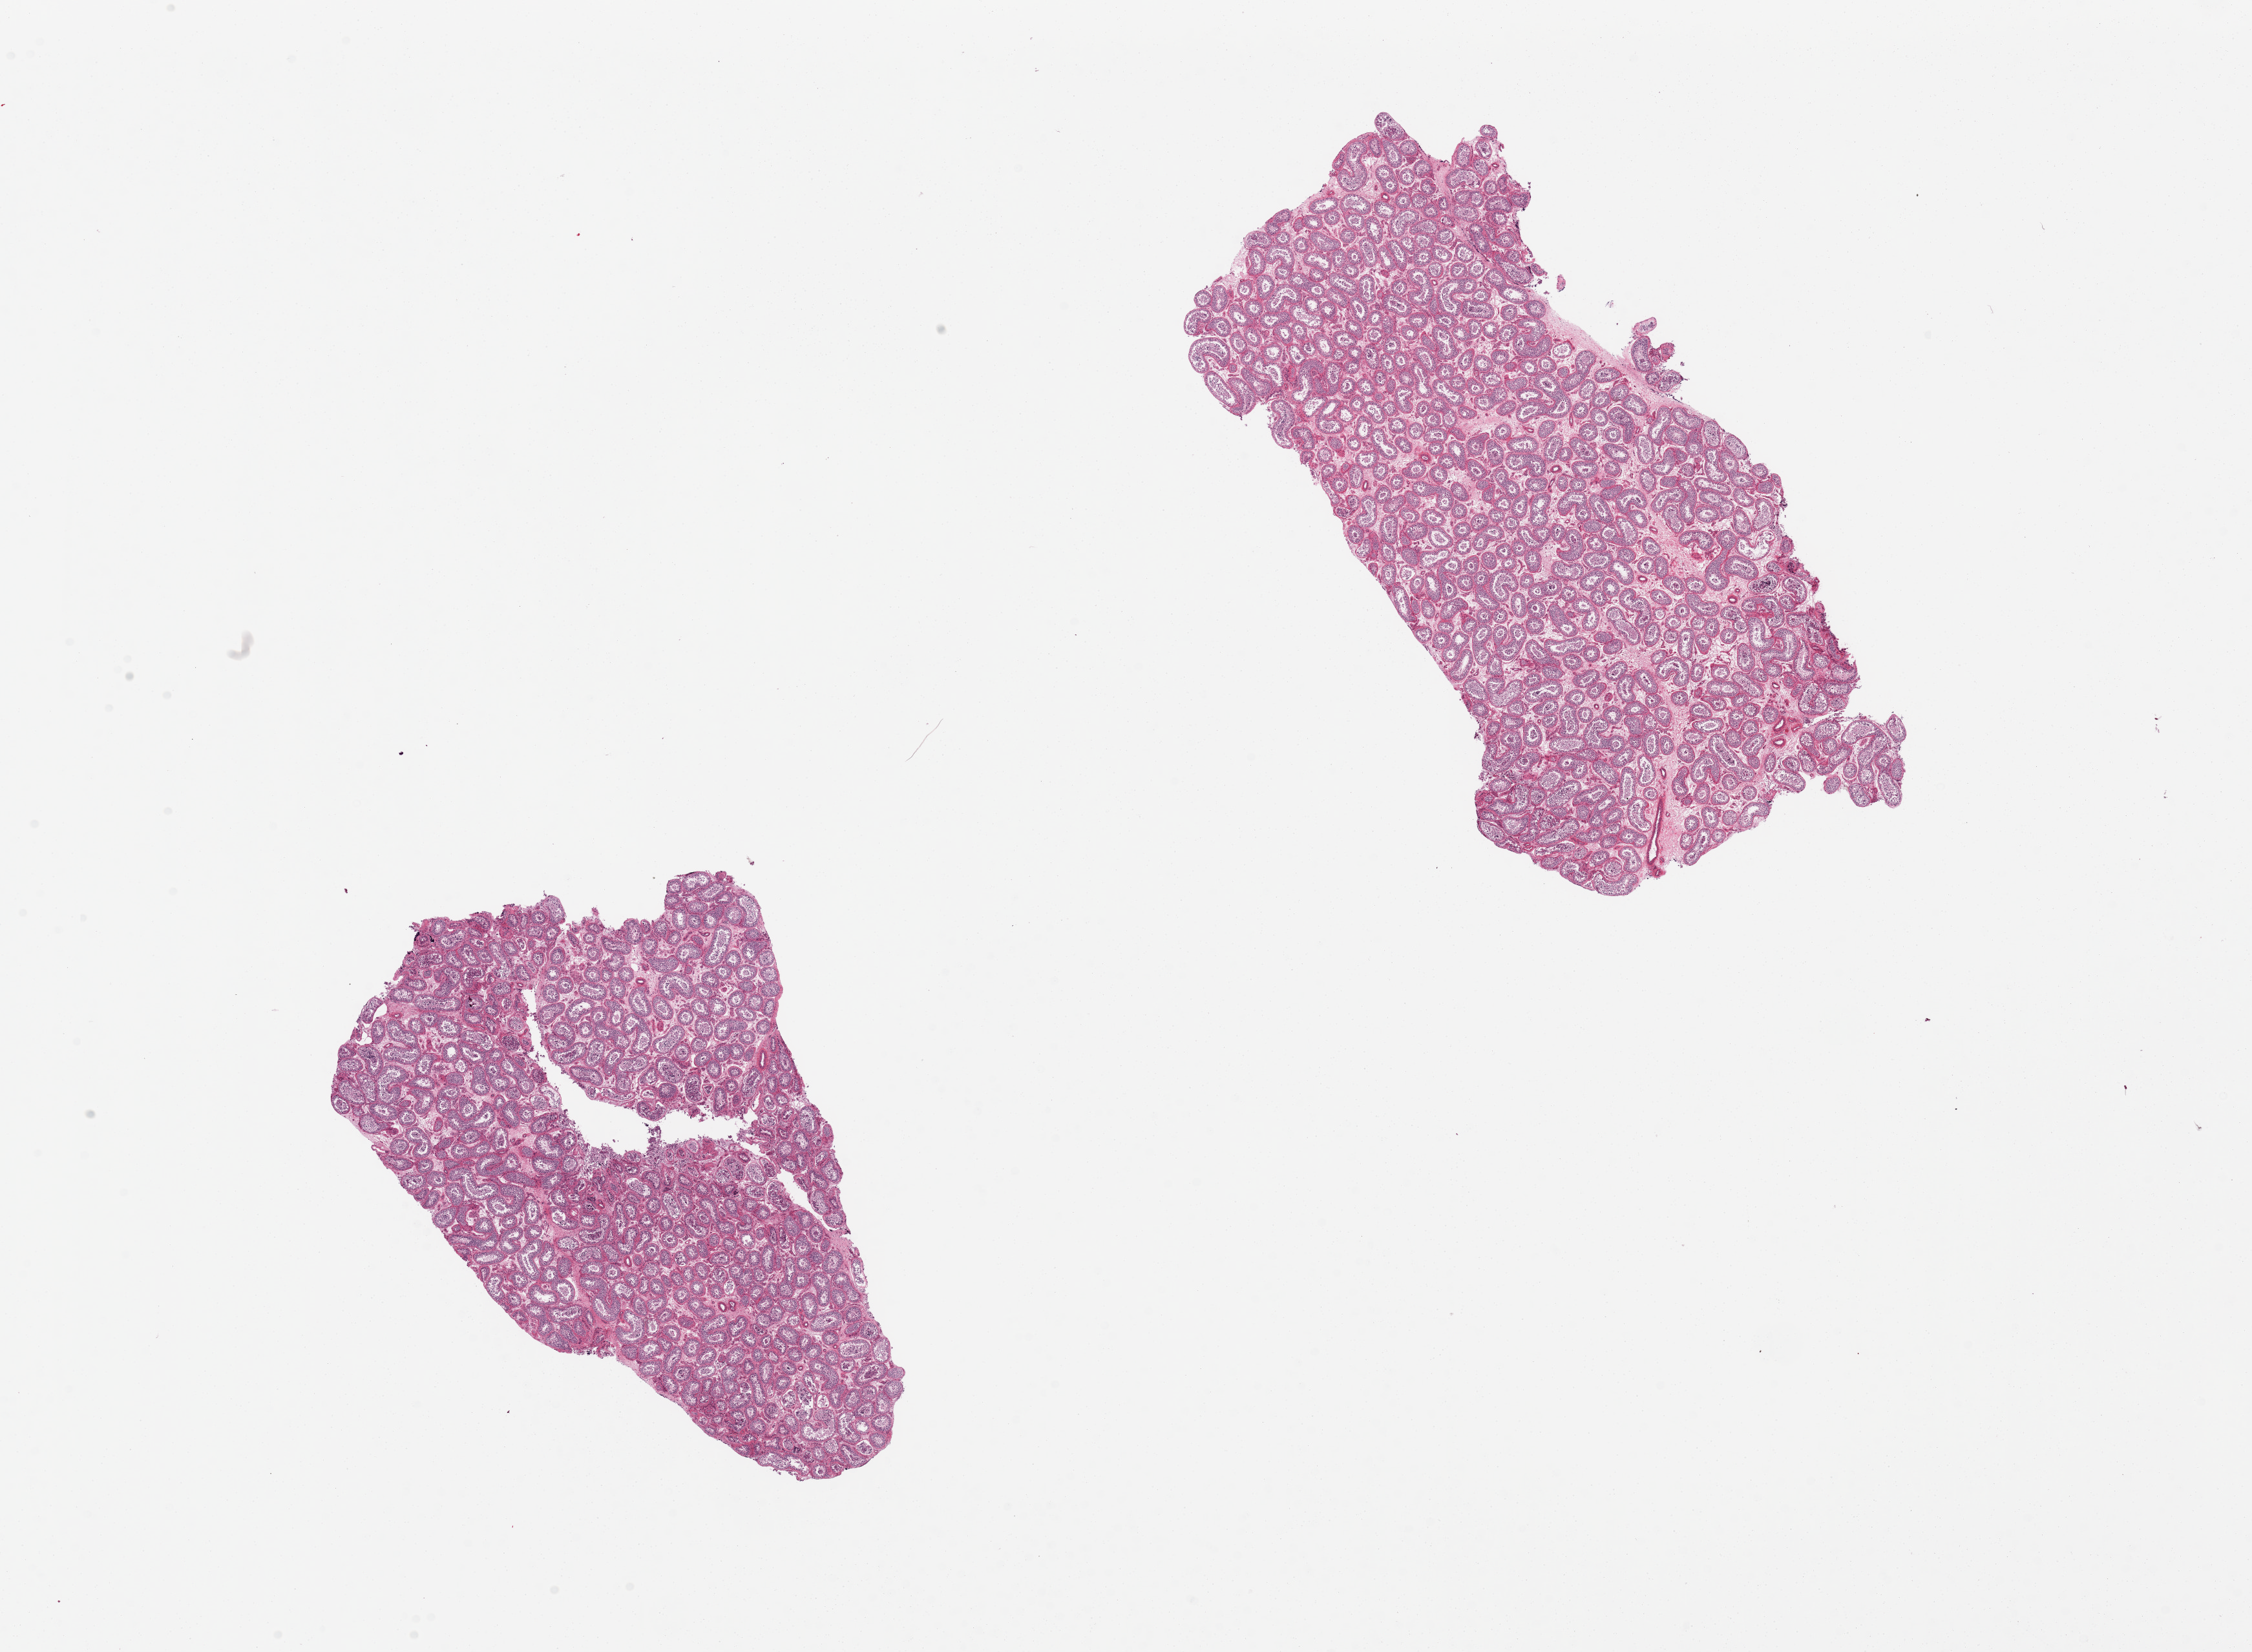
Digitized hematoxylin and eosin (H&E)-stained section, low-resolution overview of the scanned area, about 27.6 x 20.2 mm (acquisition: 20x scan); PAXgene-fixed paraffin-embedded (PFPE) section; sampled site (target tissue): testis; tissue donor sample. Male donor.
• pathologist's review note for this sample: 2 pieces; active spermatogenesis